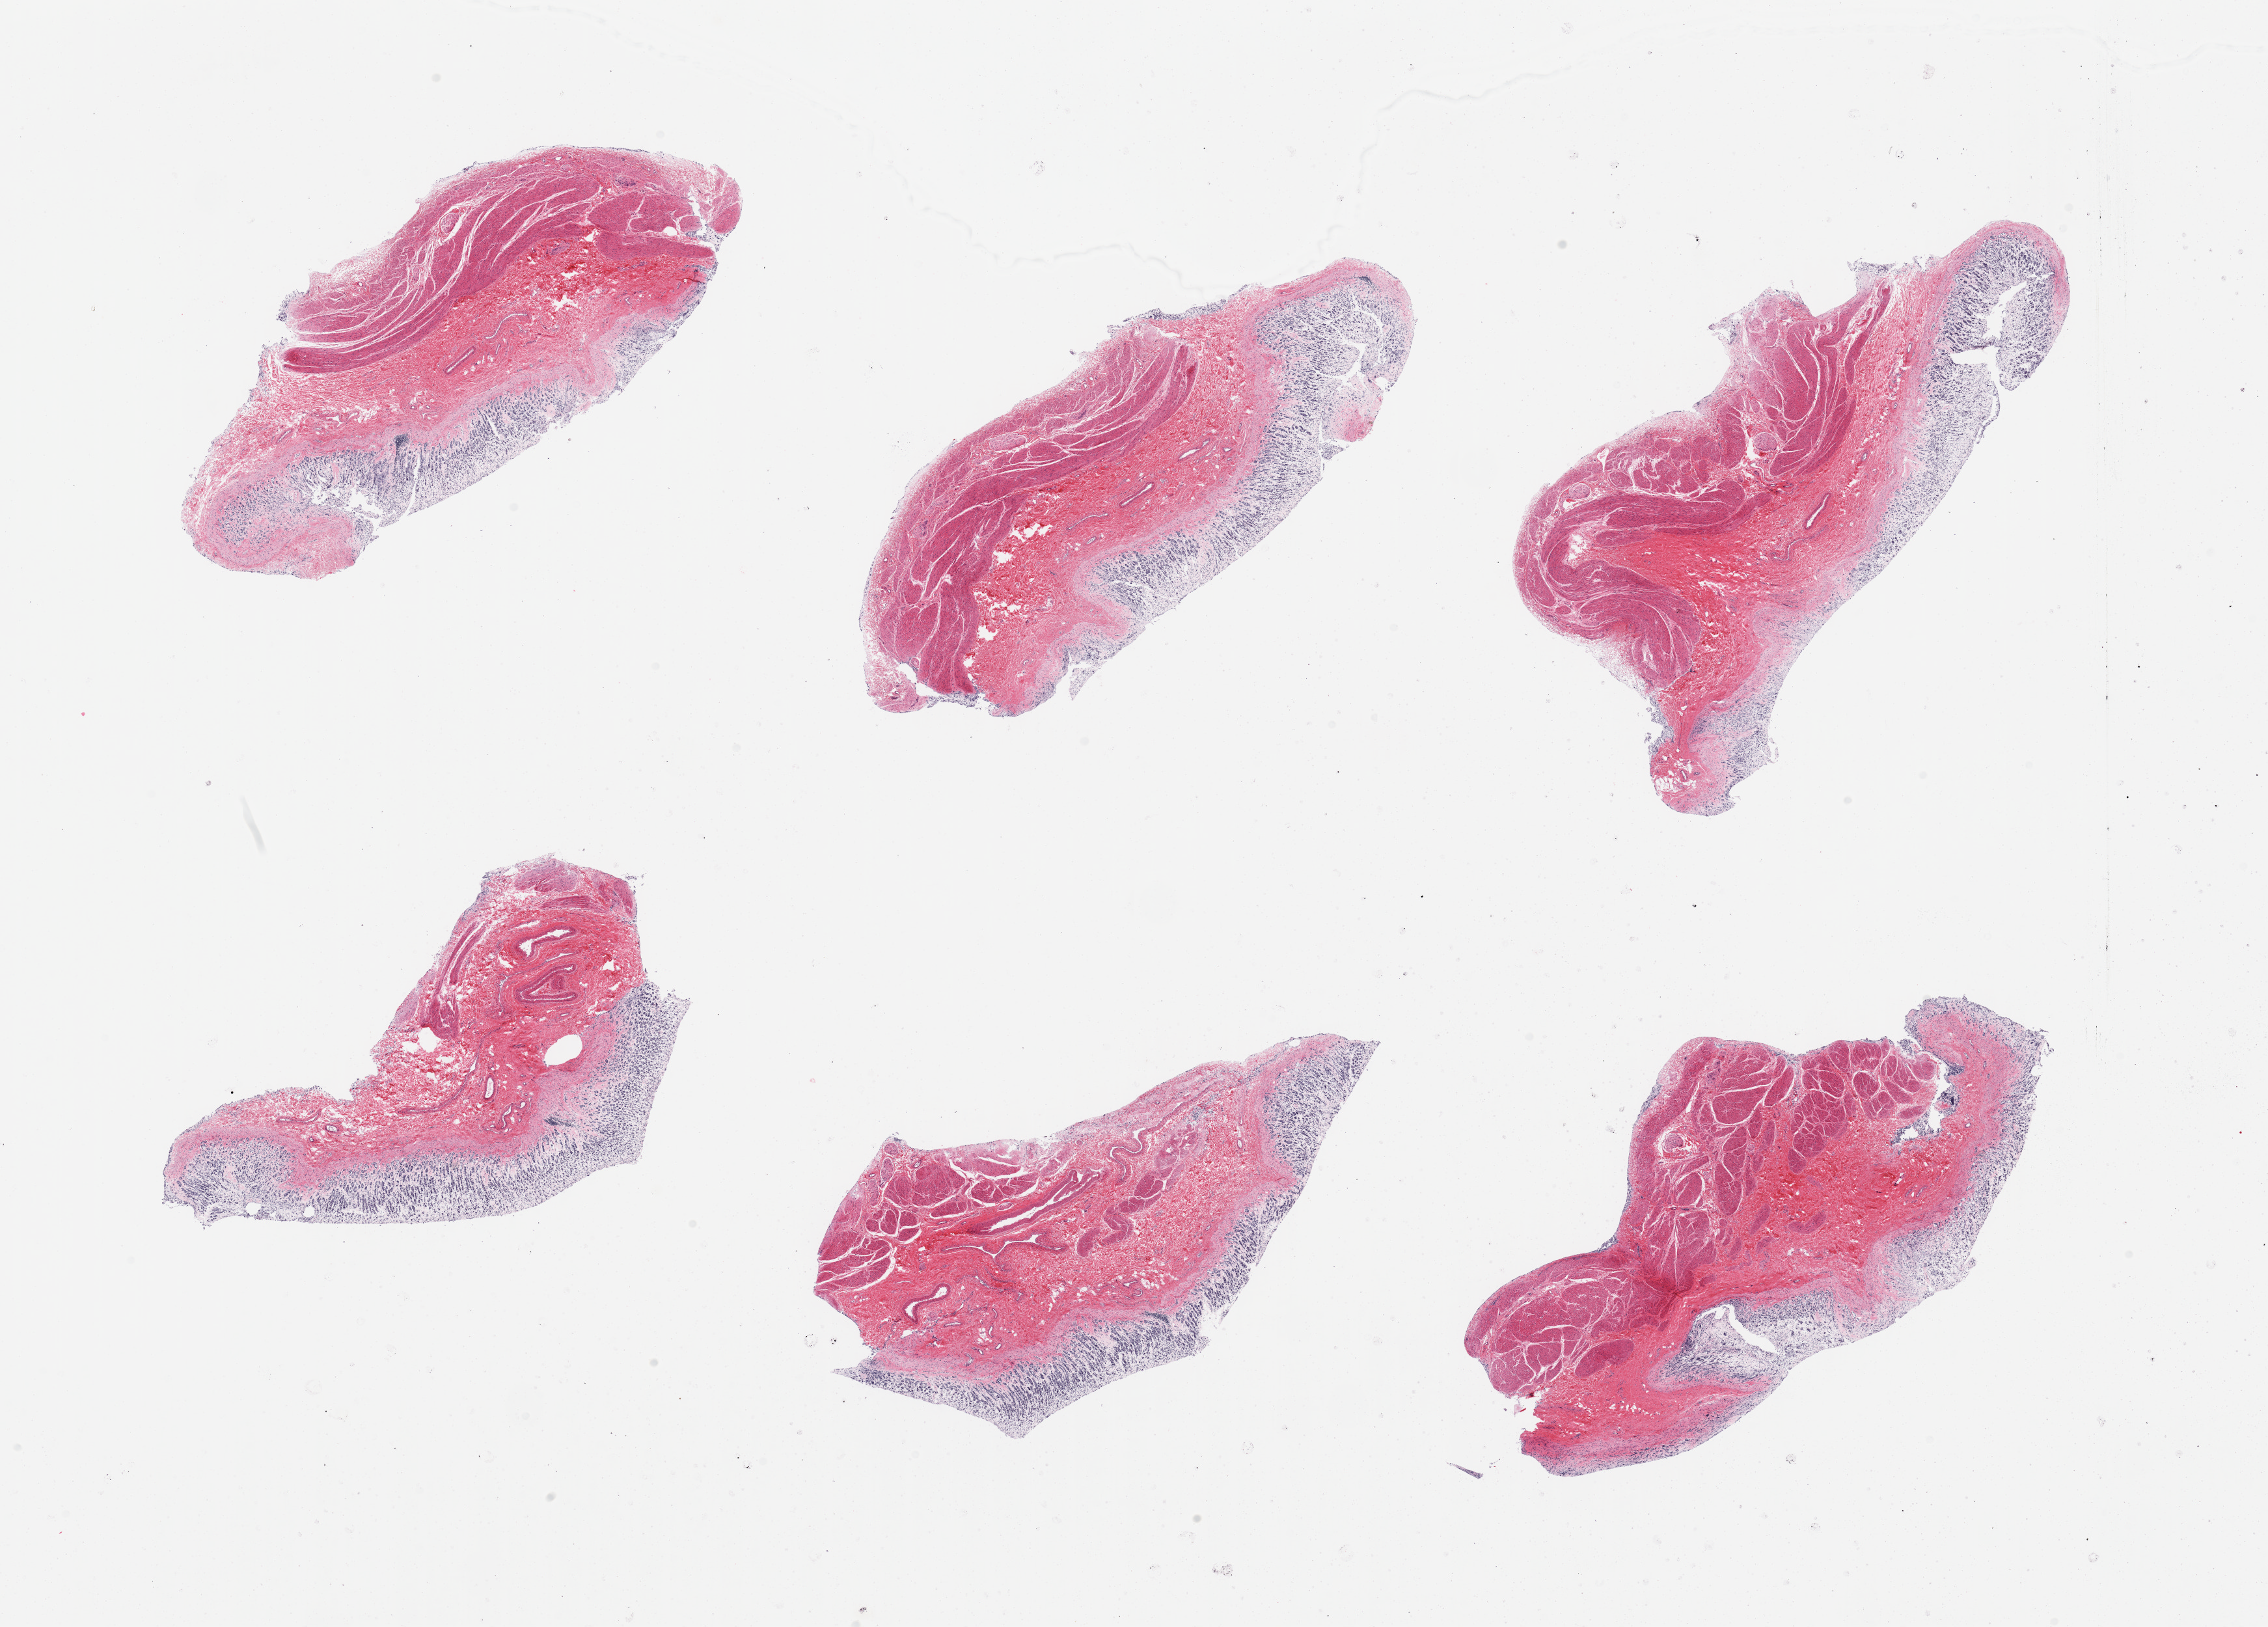
Digitized hematoxylin and eosin (H&E)-stained section, whole scanned area (about 27.6 x 19.8 mm, slide scanned at 20x) shown as a low-resolution overview. PAXgene-fixed paraffin-embedded (PFPE) section. Target tissue: stomach. Tissue donor sample. Female donor.
* pathologist's review note for this sample: 6 pieces; mucosa autolyzed, muscularis preserved